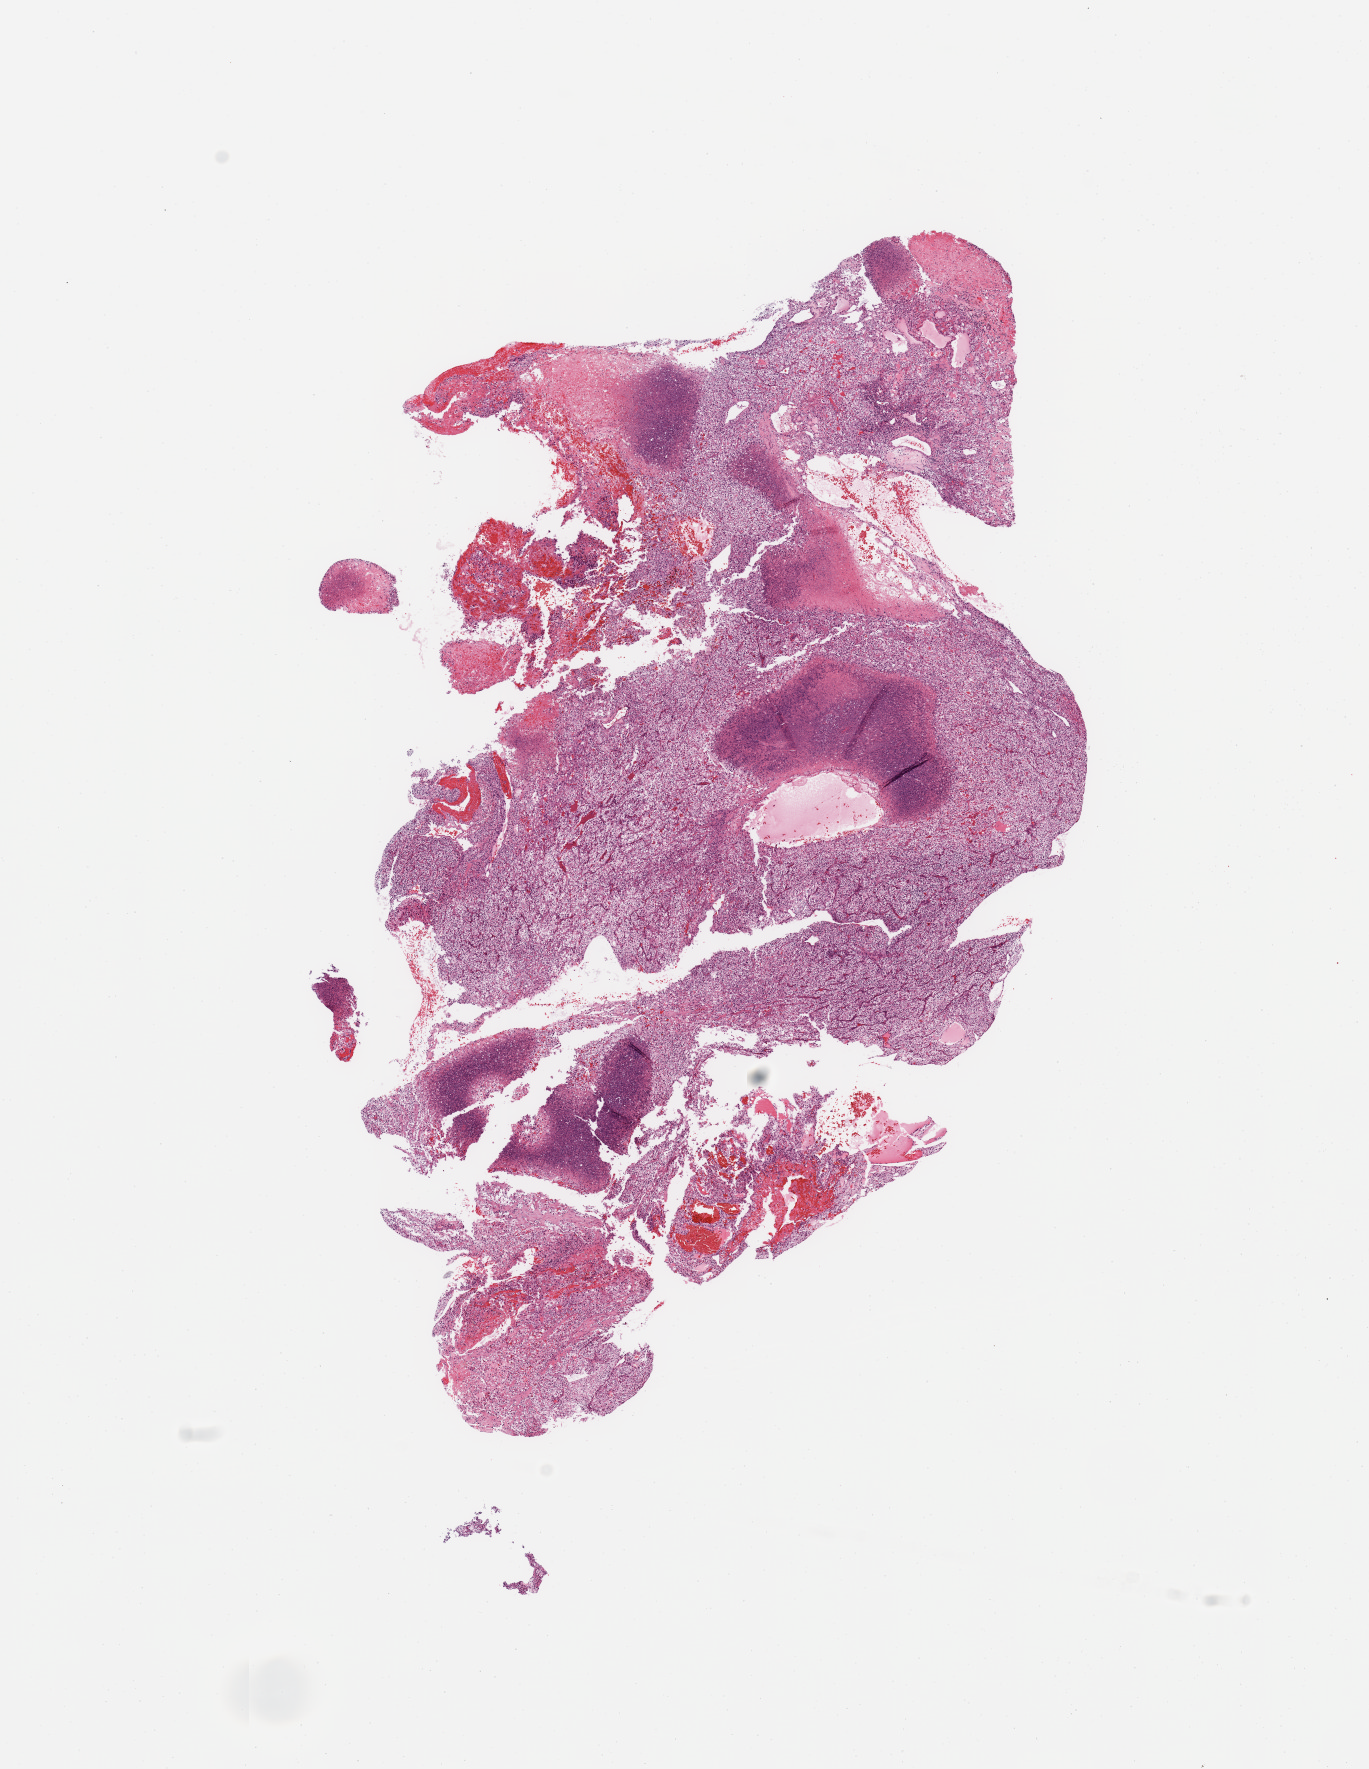
Whole-slide histology image, H&E-stained — whole scanned area (about 10.8 x 14.0 mm) shown as a low-resolution overview; tumour tissue sample, sampled site: kidney. 71-year-old female patient. Composition of this section per pathologist review: tumour nuclei 80%, necrosis 15%.
Histologic diagnosis: Renal cell carcinoma, NOS.